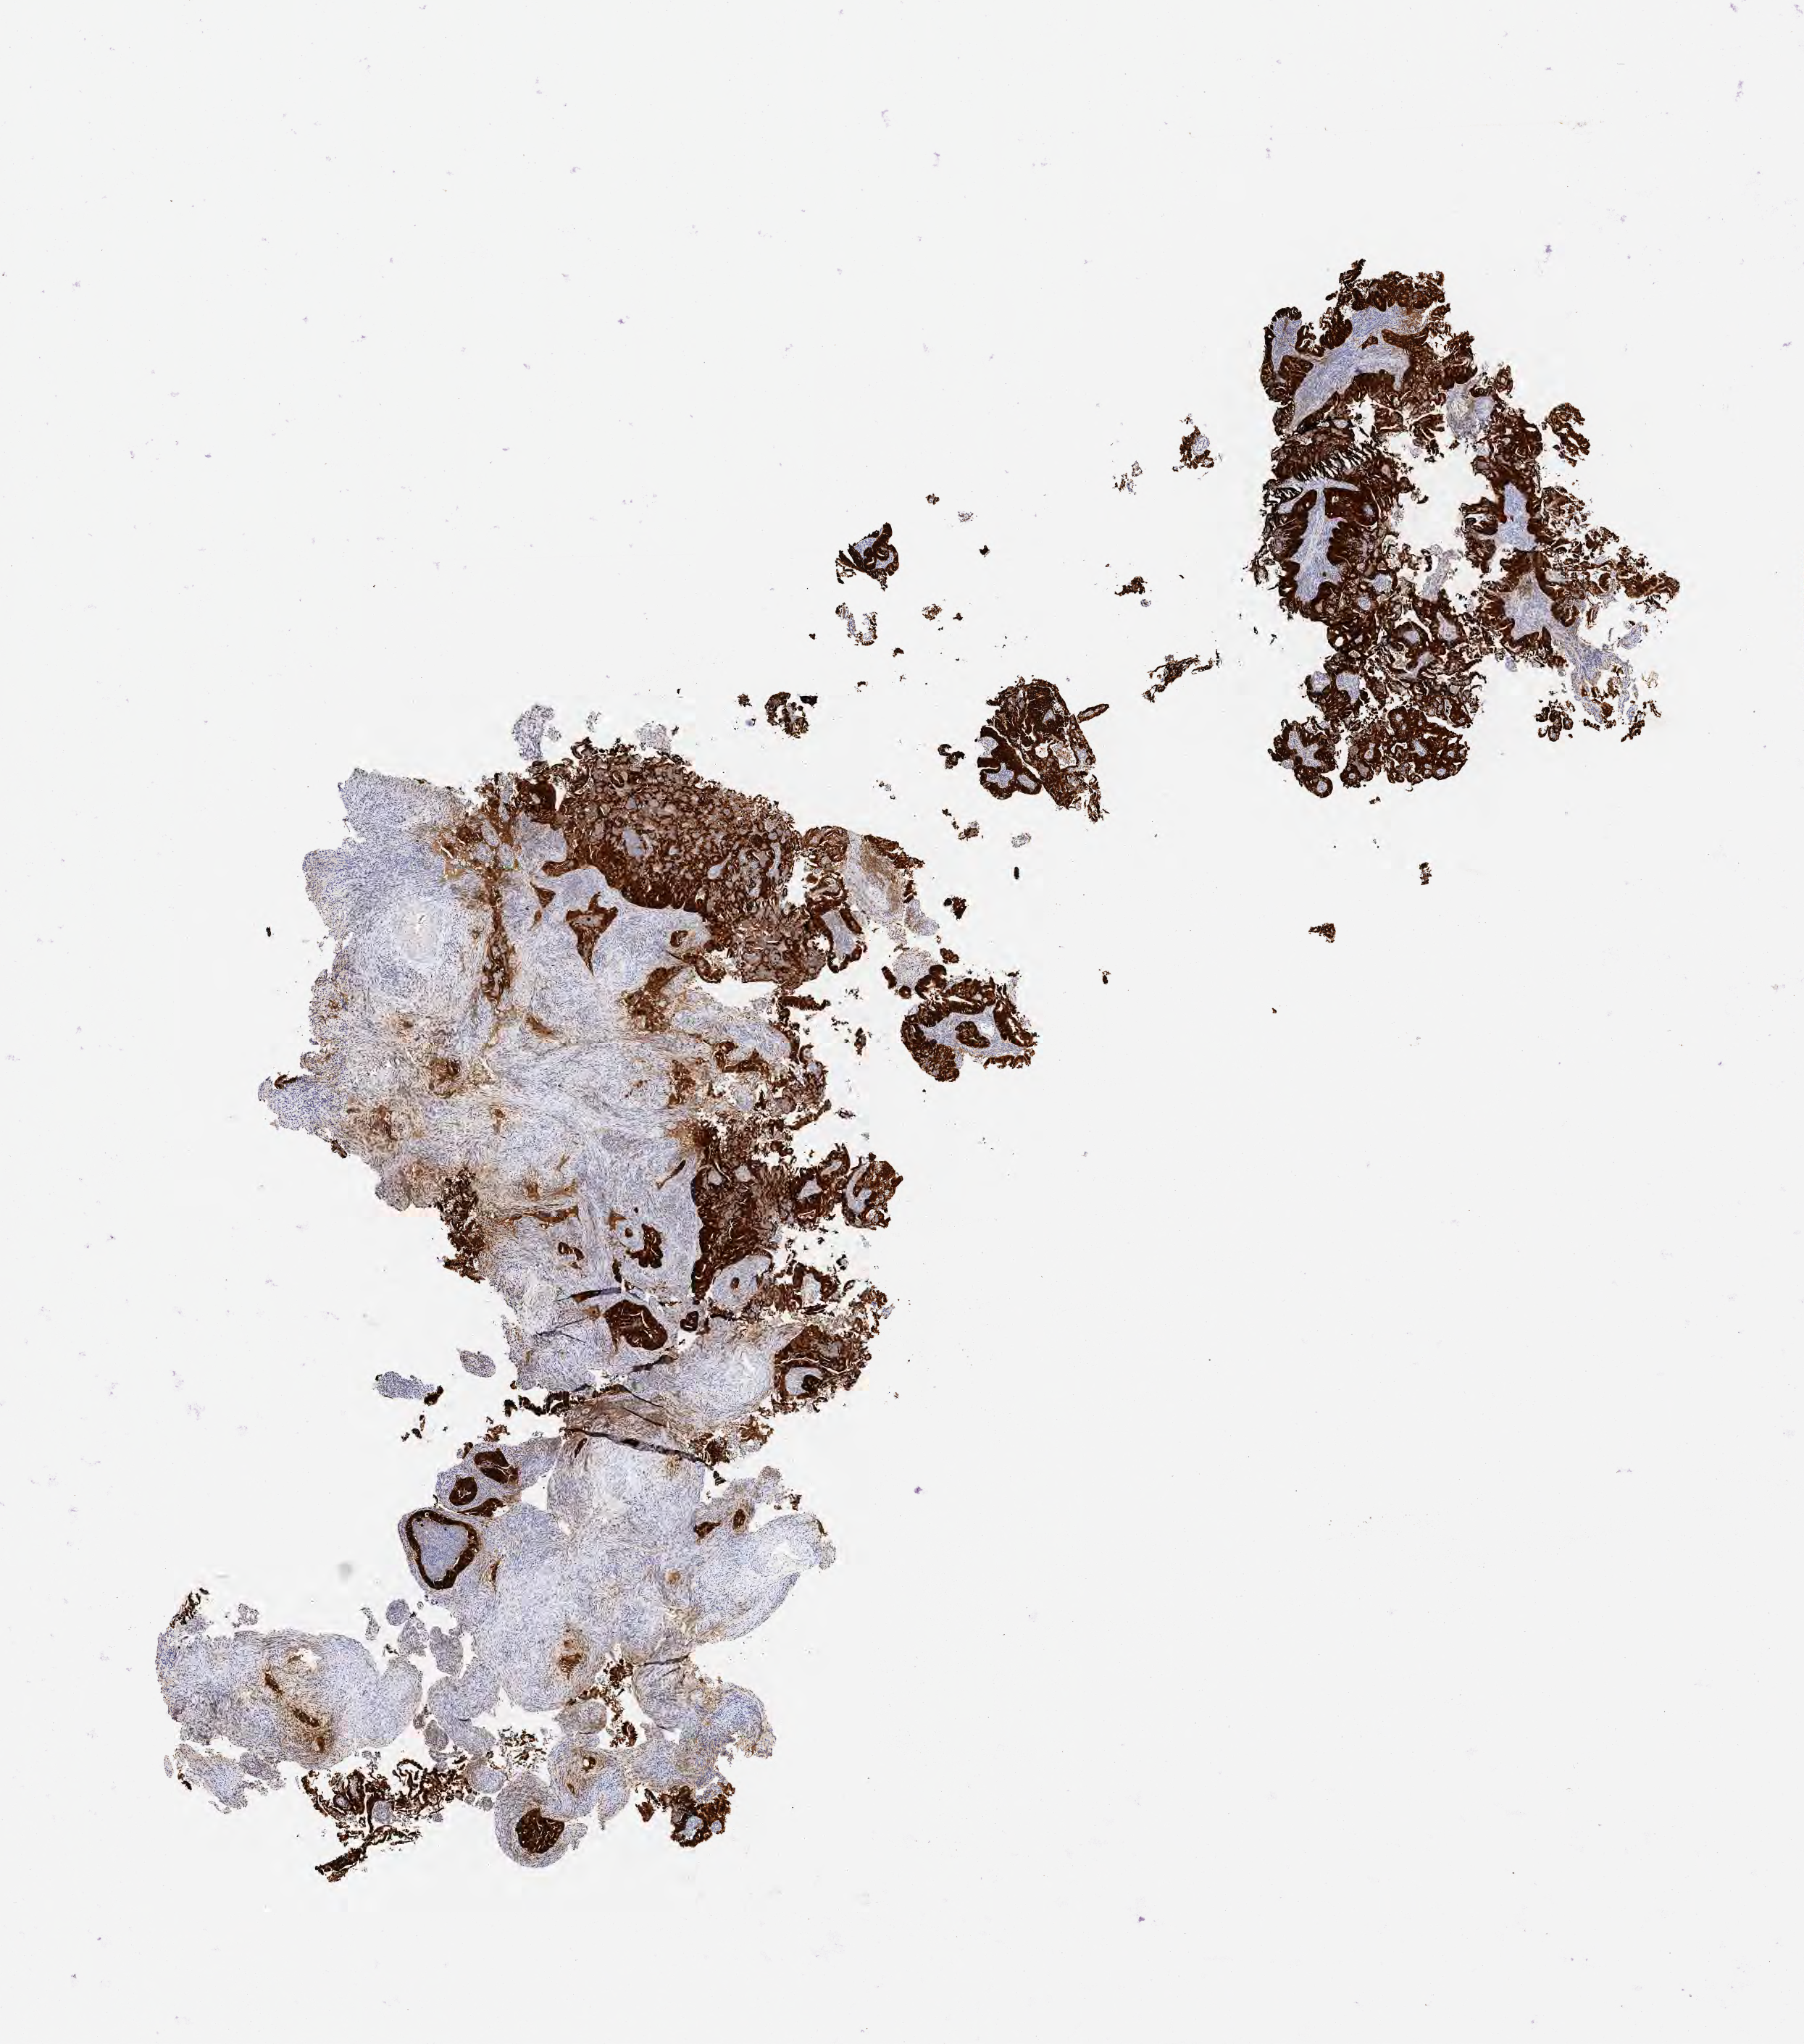
Whole-slide image, immunohistochemical stain for p16 (p16INK4a) — low-resolution overview of the scanned area, about 10.1 x 11.4 mm. Specimen: tumor tissue. Site: cervix. Patient: female, 42 years old.
• diagnosis: Adenocarcinoma, NOS